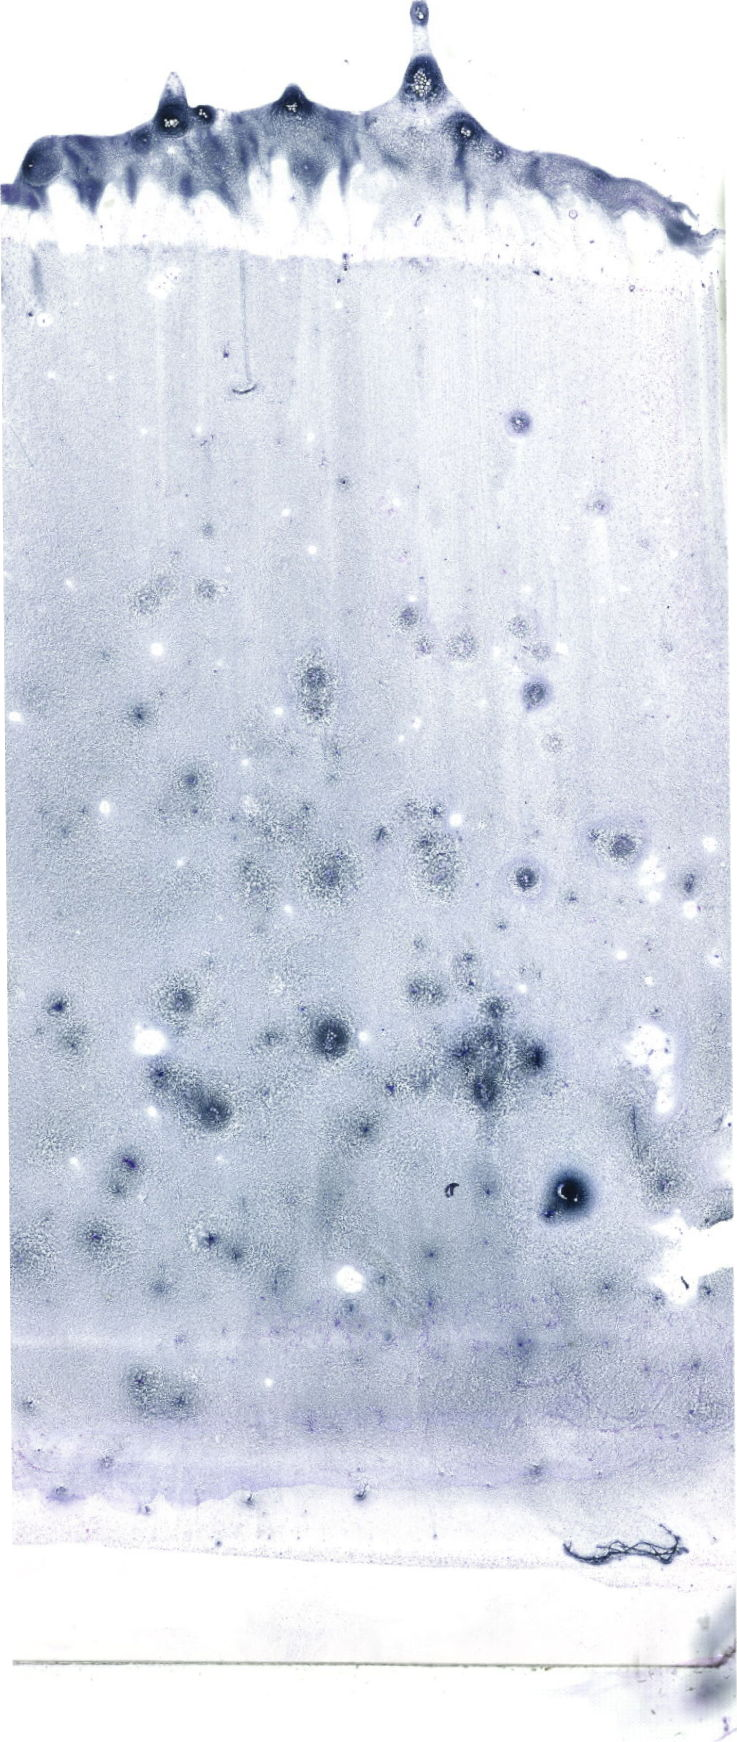
Whole-slide image of a May-Grünwald-Giemsa (MGG)-stained bone marrow aspirate smear, low-resolution overview of the scanned area, about 20.9 x 49.4 mm. Male patient.
Diagnosis: B Acute Lymphoblastic Leukemia.